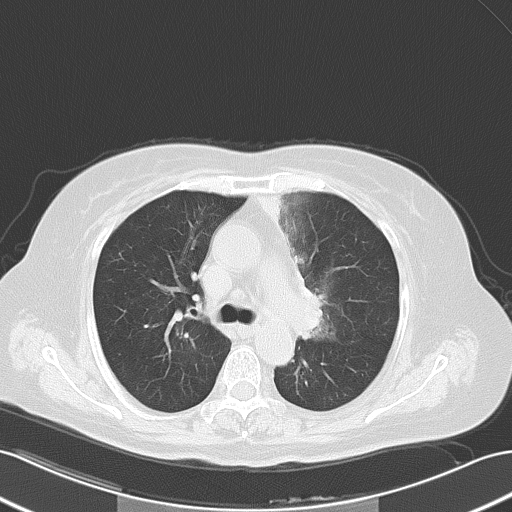
Chest CT, one axial slice; slice 37 of 56 in the series (ordered by position); 120 kVp; lung window (W 1500 / L -600 HU); 5 mm slice thickness; 512 × 512 image matrix. Female patient, age 65 years. Case-level facts recorded for this patient, not image findings: clinical TNM (as recorded): T2b N1 M0.
Outlined on this slice (bounding box drawn by a radiologist):
- lung tumour (recorded histology: adenocarcinoma): bounding box [x1, y1, x2, y2] px = [298, 265, 335, 341]